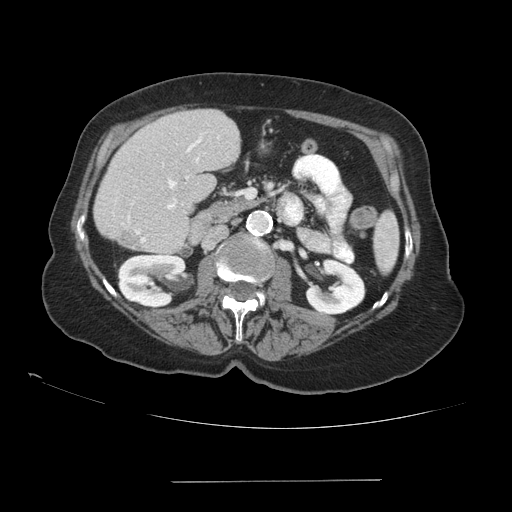
Contrast-enhanced abdominal CT (liver protocol), one axial slice. Position 38 of 89 along the scan axis. Soft-tissue window (W 400 / L 40 HU). 512 × 512 image matrix. Case-level facts recorded for this patient, not image findings: diagnosis: hepatocellular carcinoma (patient treated with transarterial chemoembolisation; whether this scan precedes or follows treatment is not stated here); TNM stage (as recorded): Stage-IVA; Child-Pugh class: A; tumour differentiation: poorly differentiated; tumour nodularity: uninodular.
Outlined on this slice (semi-automatically segmented with operator editing):
- liver parenchyma outside the tumour (the mass and vessels are separate outlines, so this box may not span the whole liver): box from (x=93, y=109) to (x=240, y=256) px
- liver vessels: (x=128, y=137)–(x=201, y=242)